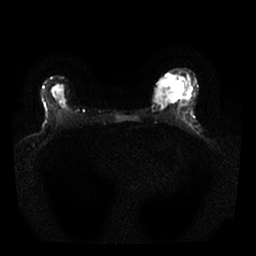
Breast MRI, one axial slice. Diffusion-weighted series; image 2 of 4 stored at this slice position (different b-values; order by instance number). 1.5 T. 256 × 256 image matrix, field of view 310 × 310 mm. Female patient.
Annotated regions visible in this slice (manually delineated by an expert):
- tumour on diffusion-weighted imaging: bounding box (x1, y1, x2, y2) in pixels: (156, 76, 182, 105)